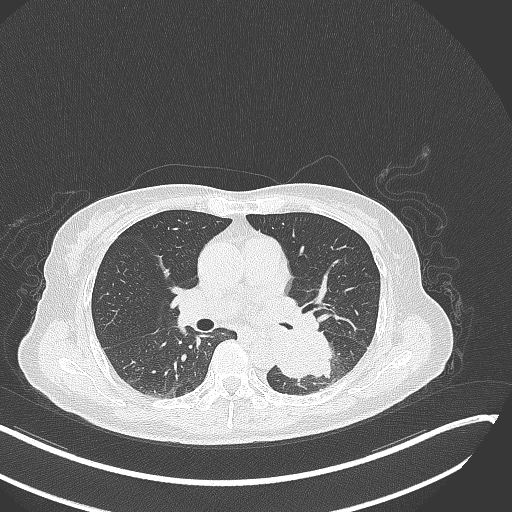
Chest CT, one axial slice; reconstruction kernel B70f; 120 kVp; lung window (W 1500 / L -600 HU); 512 × 512 image matrix, field of view 400 × 400 mm. Female patient, age 64 years. Case-level facts recorded for this patient, not image findings: clinical TNM (as recorded): T3 N1 M1; histopathological grade: G3.
Outlined on this slice (rectangle marked by the reading radiologist):
- lung tumour (recorded histology: small cell carcinoma): box from (x=269, y=324) to (x=336, y=386) px